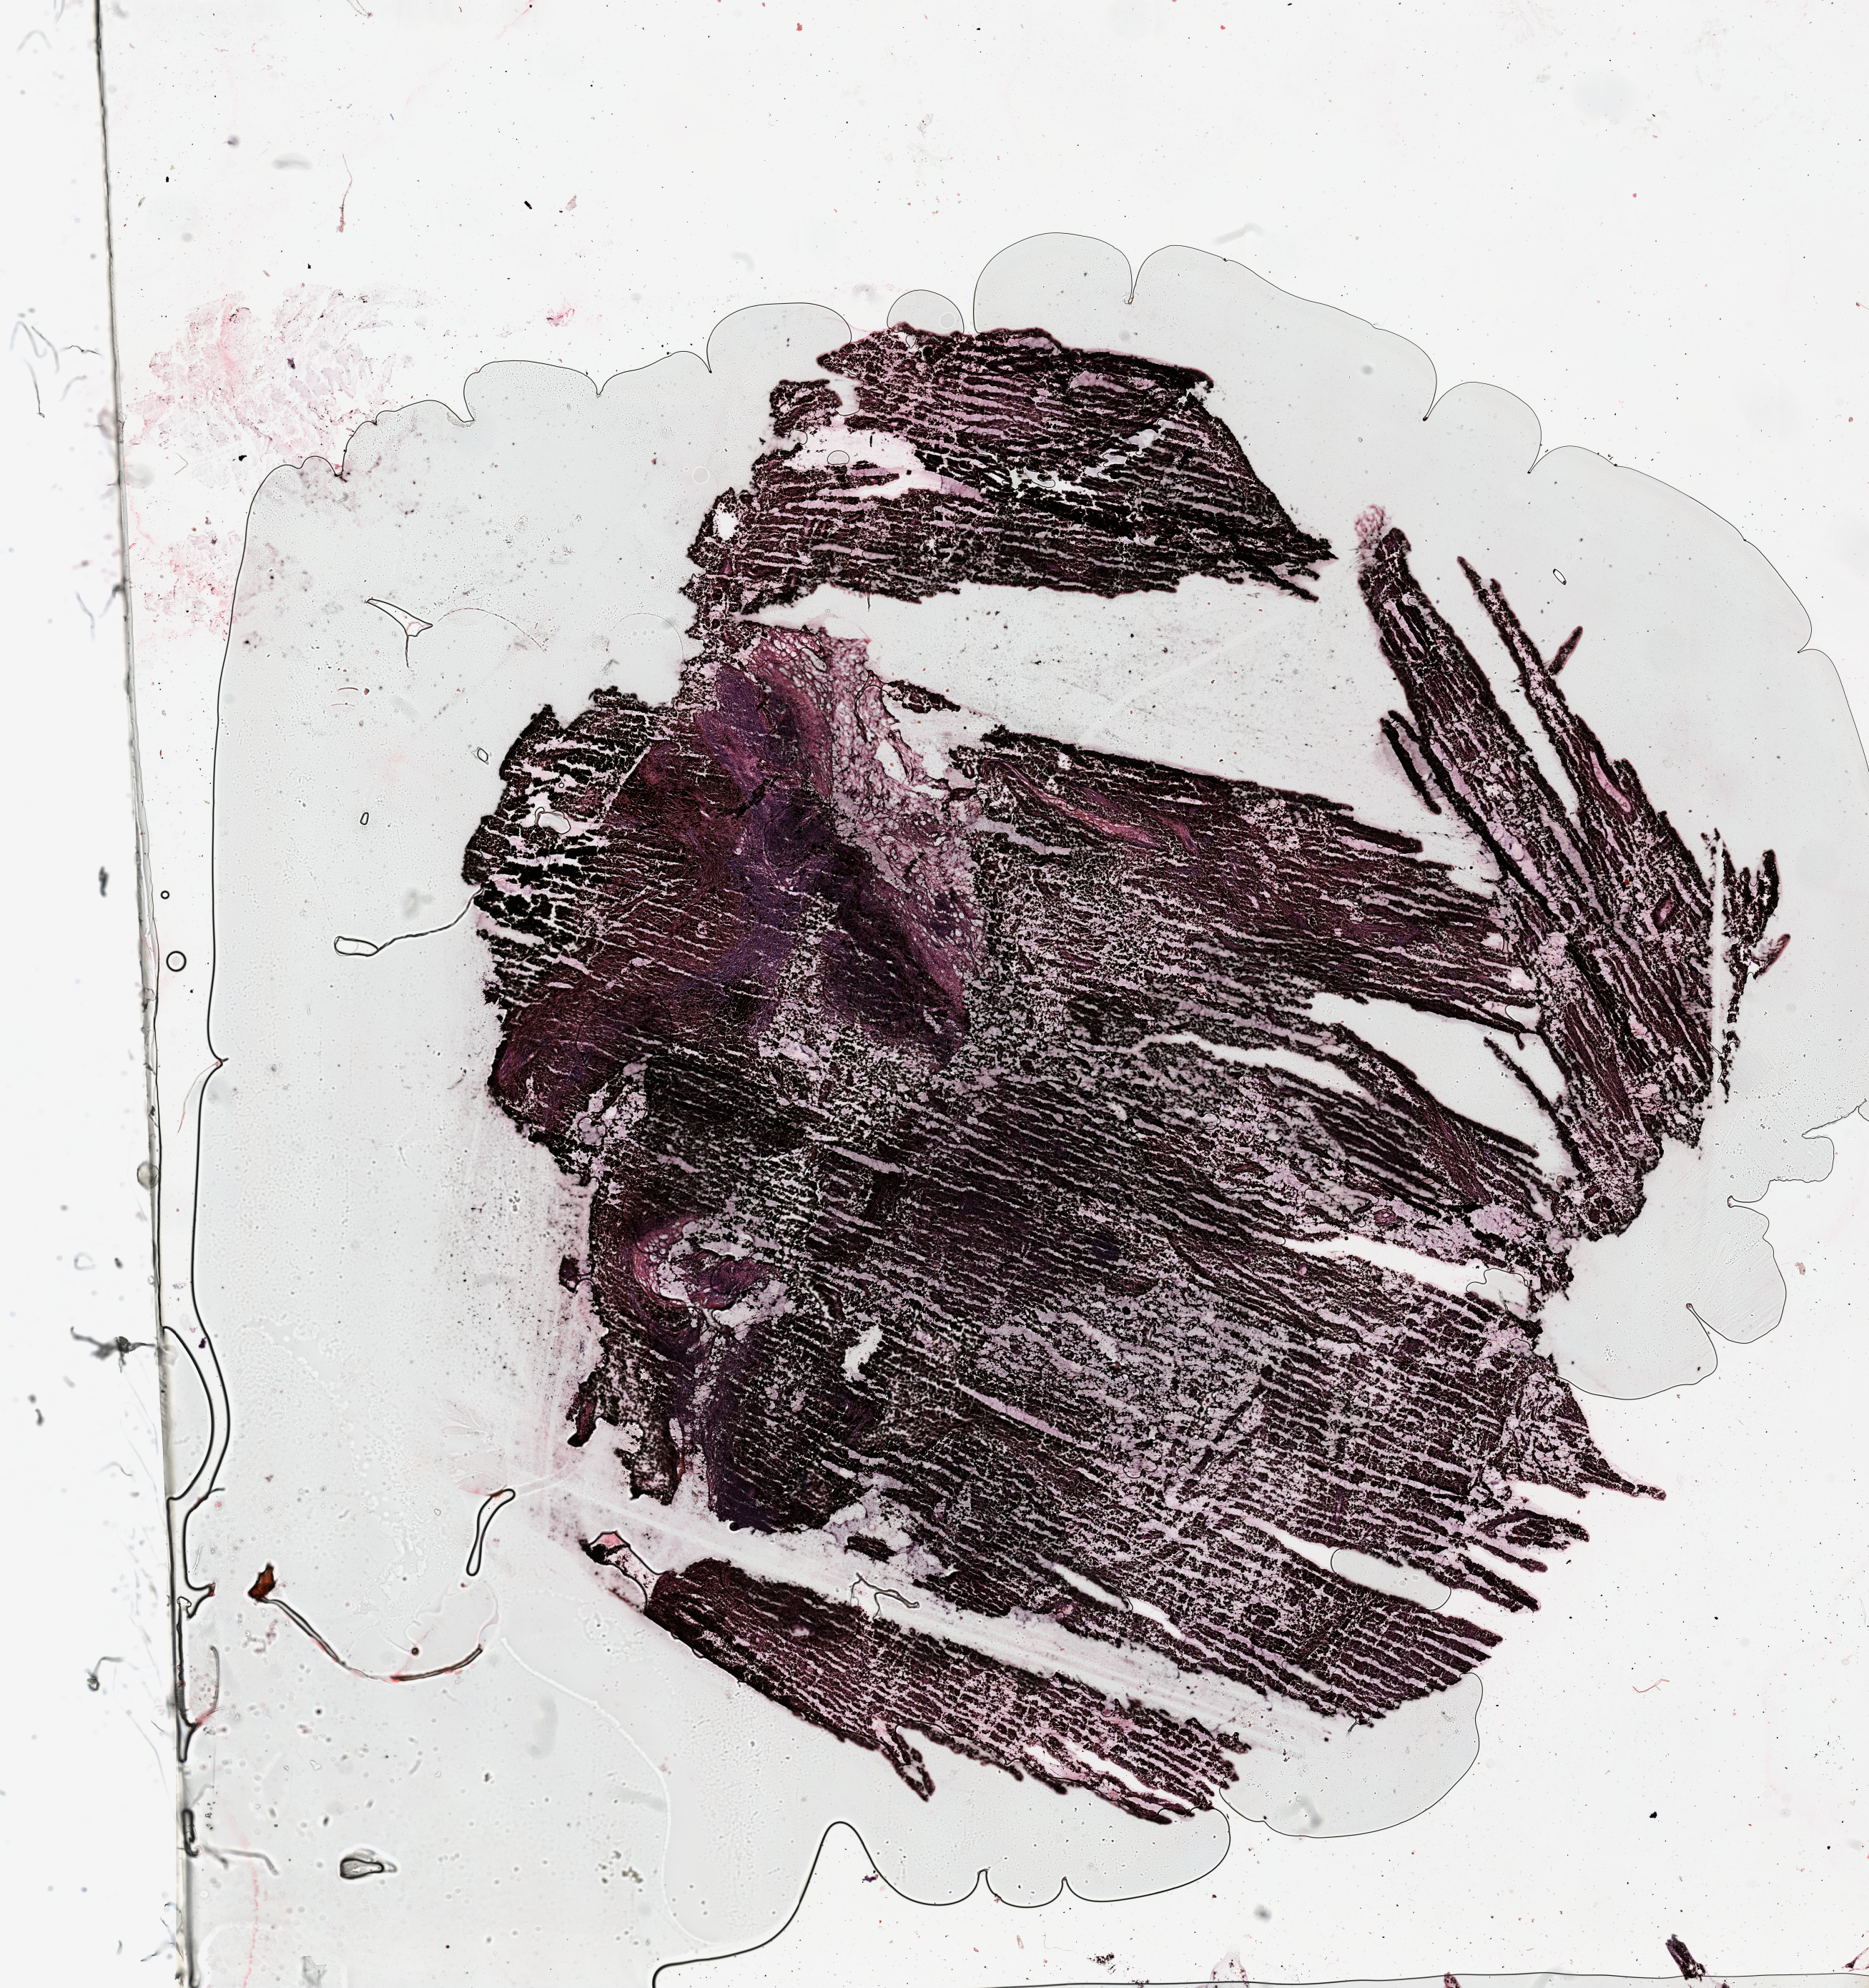
Whole-slide histology image, H&E-stained — low-resolution overview of the scanned area, about 20.7 x 22.0 mm, melanoma tumour tissue; sampled site not recorded. 74-year-old female patient.
* primary tumour site (as recorded): trunk
* patient diagnosis (cohort enrolment): cutaneous melanoma (skin)